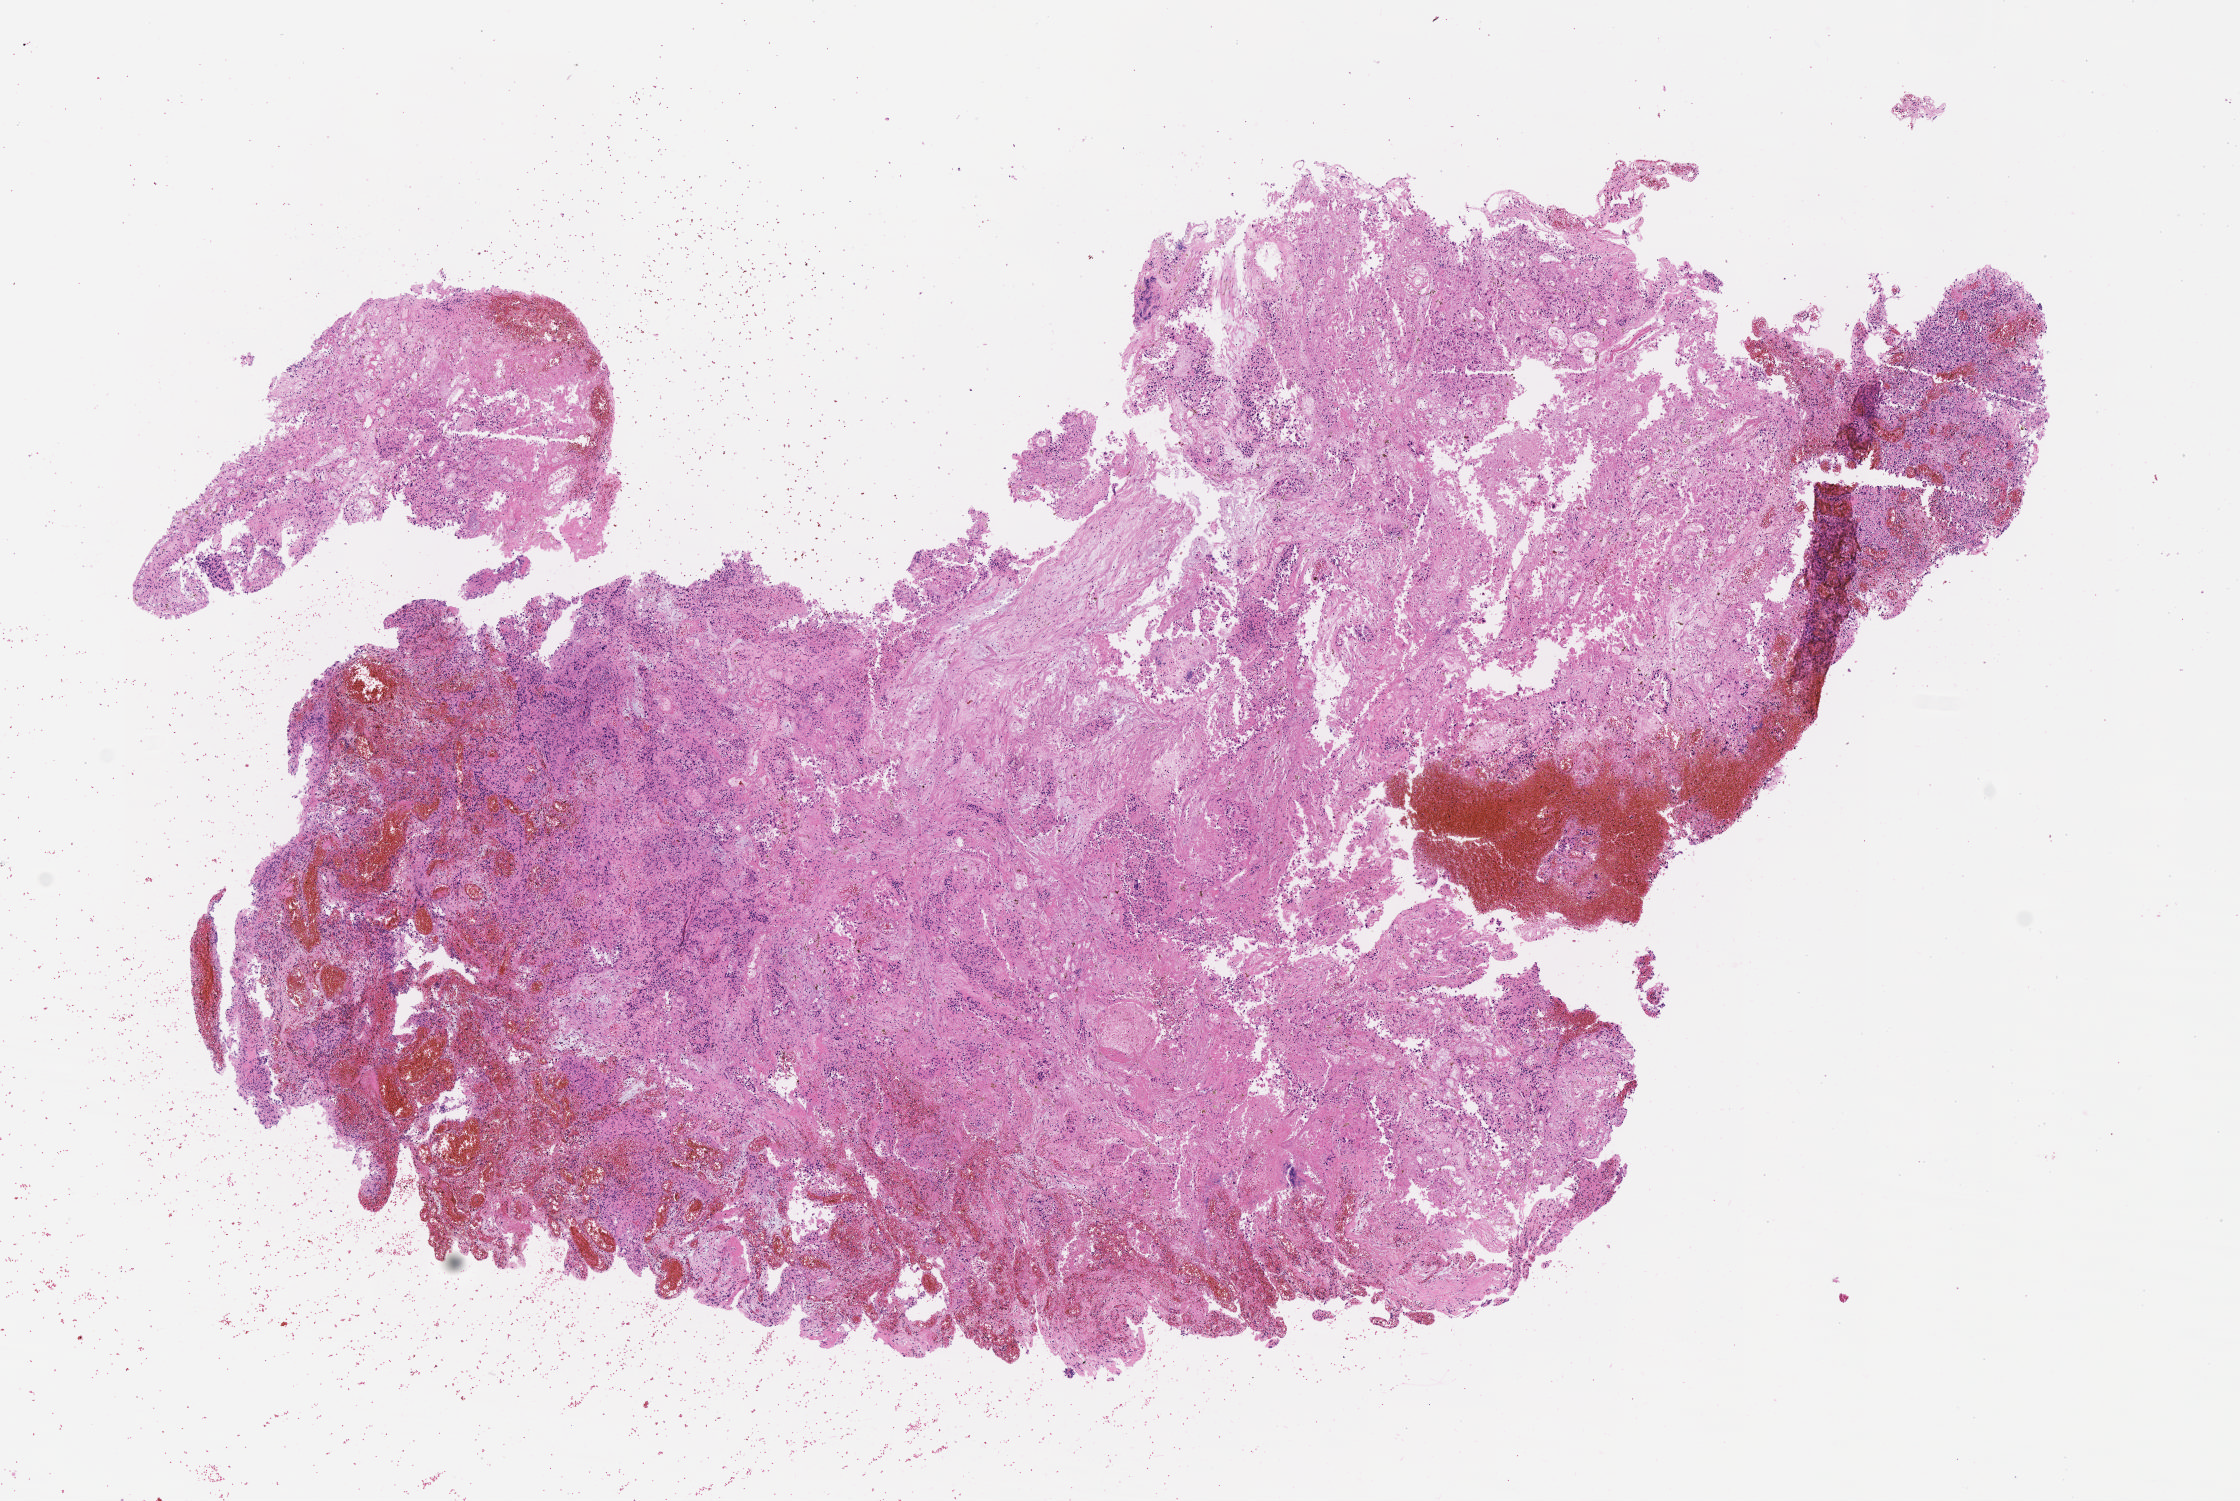
Digitized haematoxylin and eosin-stained section — whole scanned area (about 9.1 x 6.1 mm) shown as a low-resolution overview; specimen: tumor tissue; site: cervix. Female patient, aged 51.
Diagnosis: Squamous cell carcinoma, keratinizing, NOS.